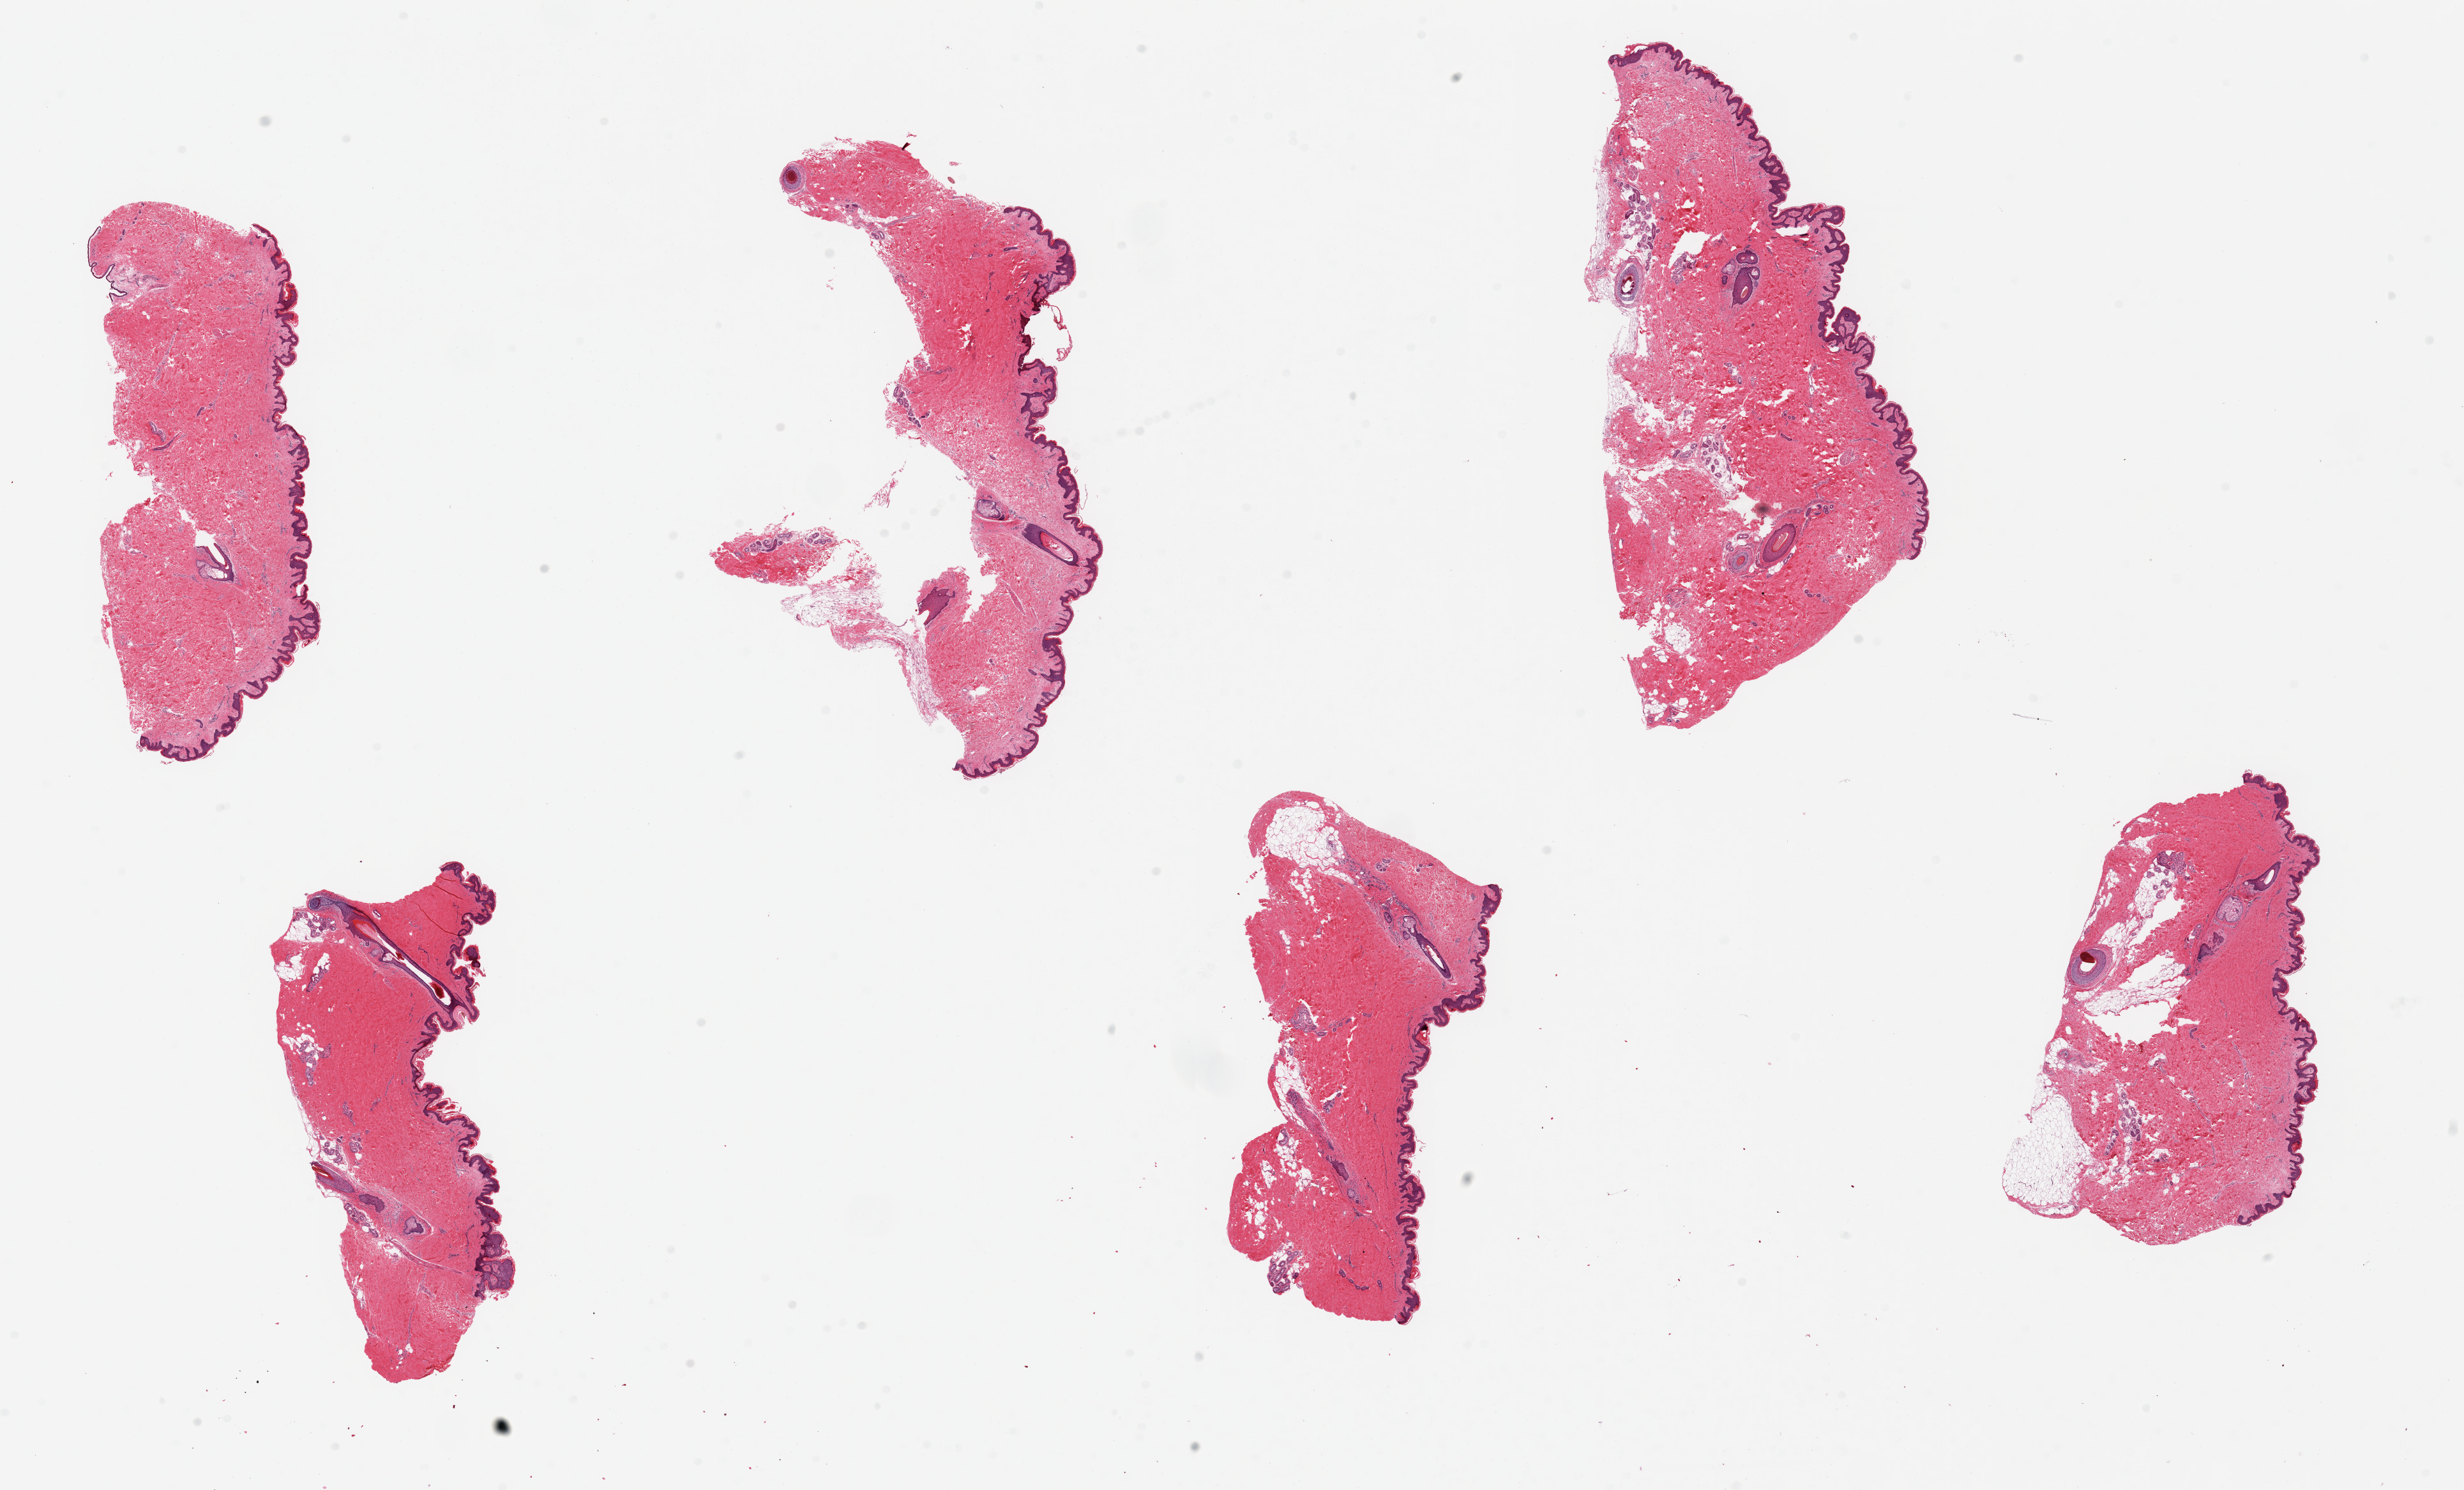
Whole-slide image, H&E stain — a low-resolution overview of the entire scanned area, about 30.5 x 18.4 mm (acquisition: 20x scan); PAXgene-fixed, paraffin-embedded tissue; target tissue: skin of suprapubic region; donor tissue sample. Donor sex: male.
Review note (as recorded): 6 pieces, up to 8x5mm; squamous epithelium is ~1% thickness.